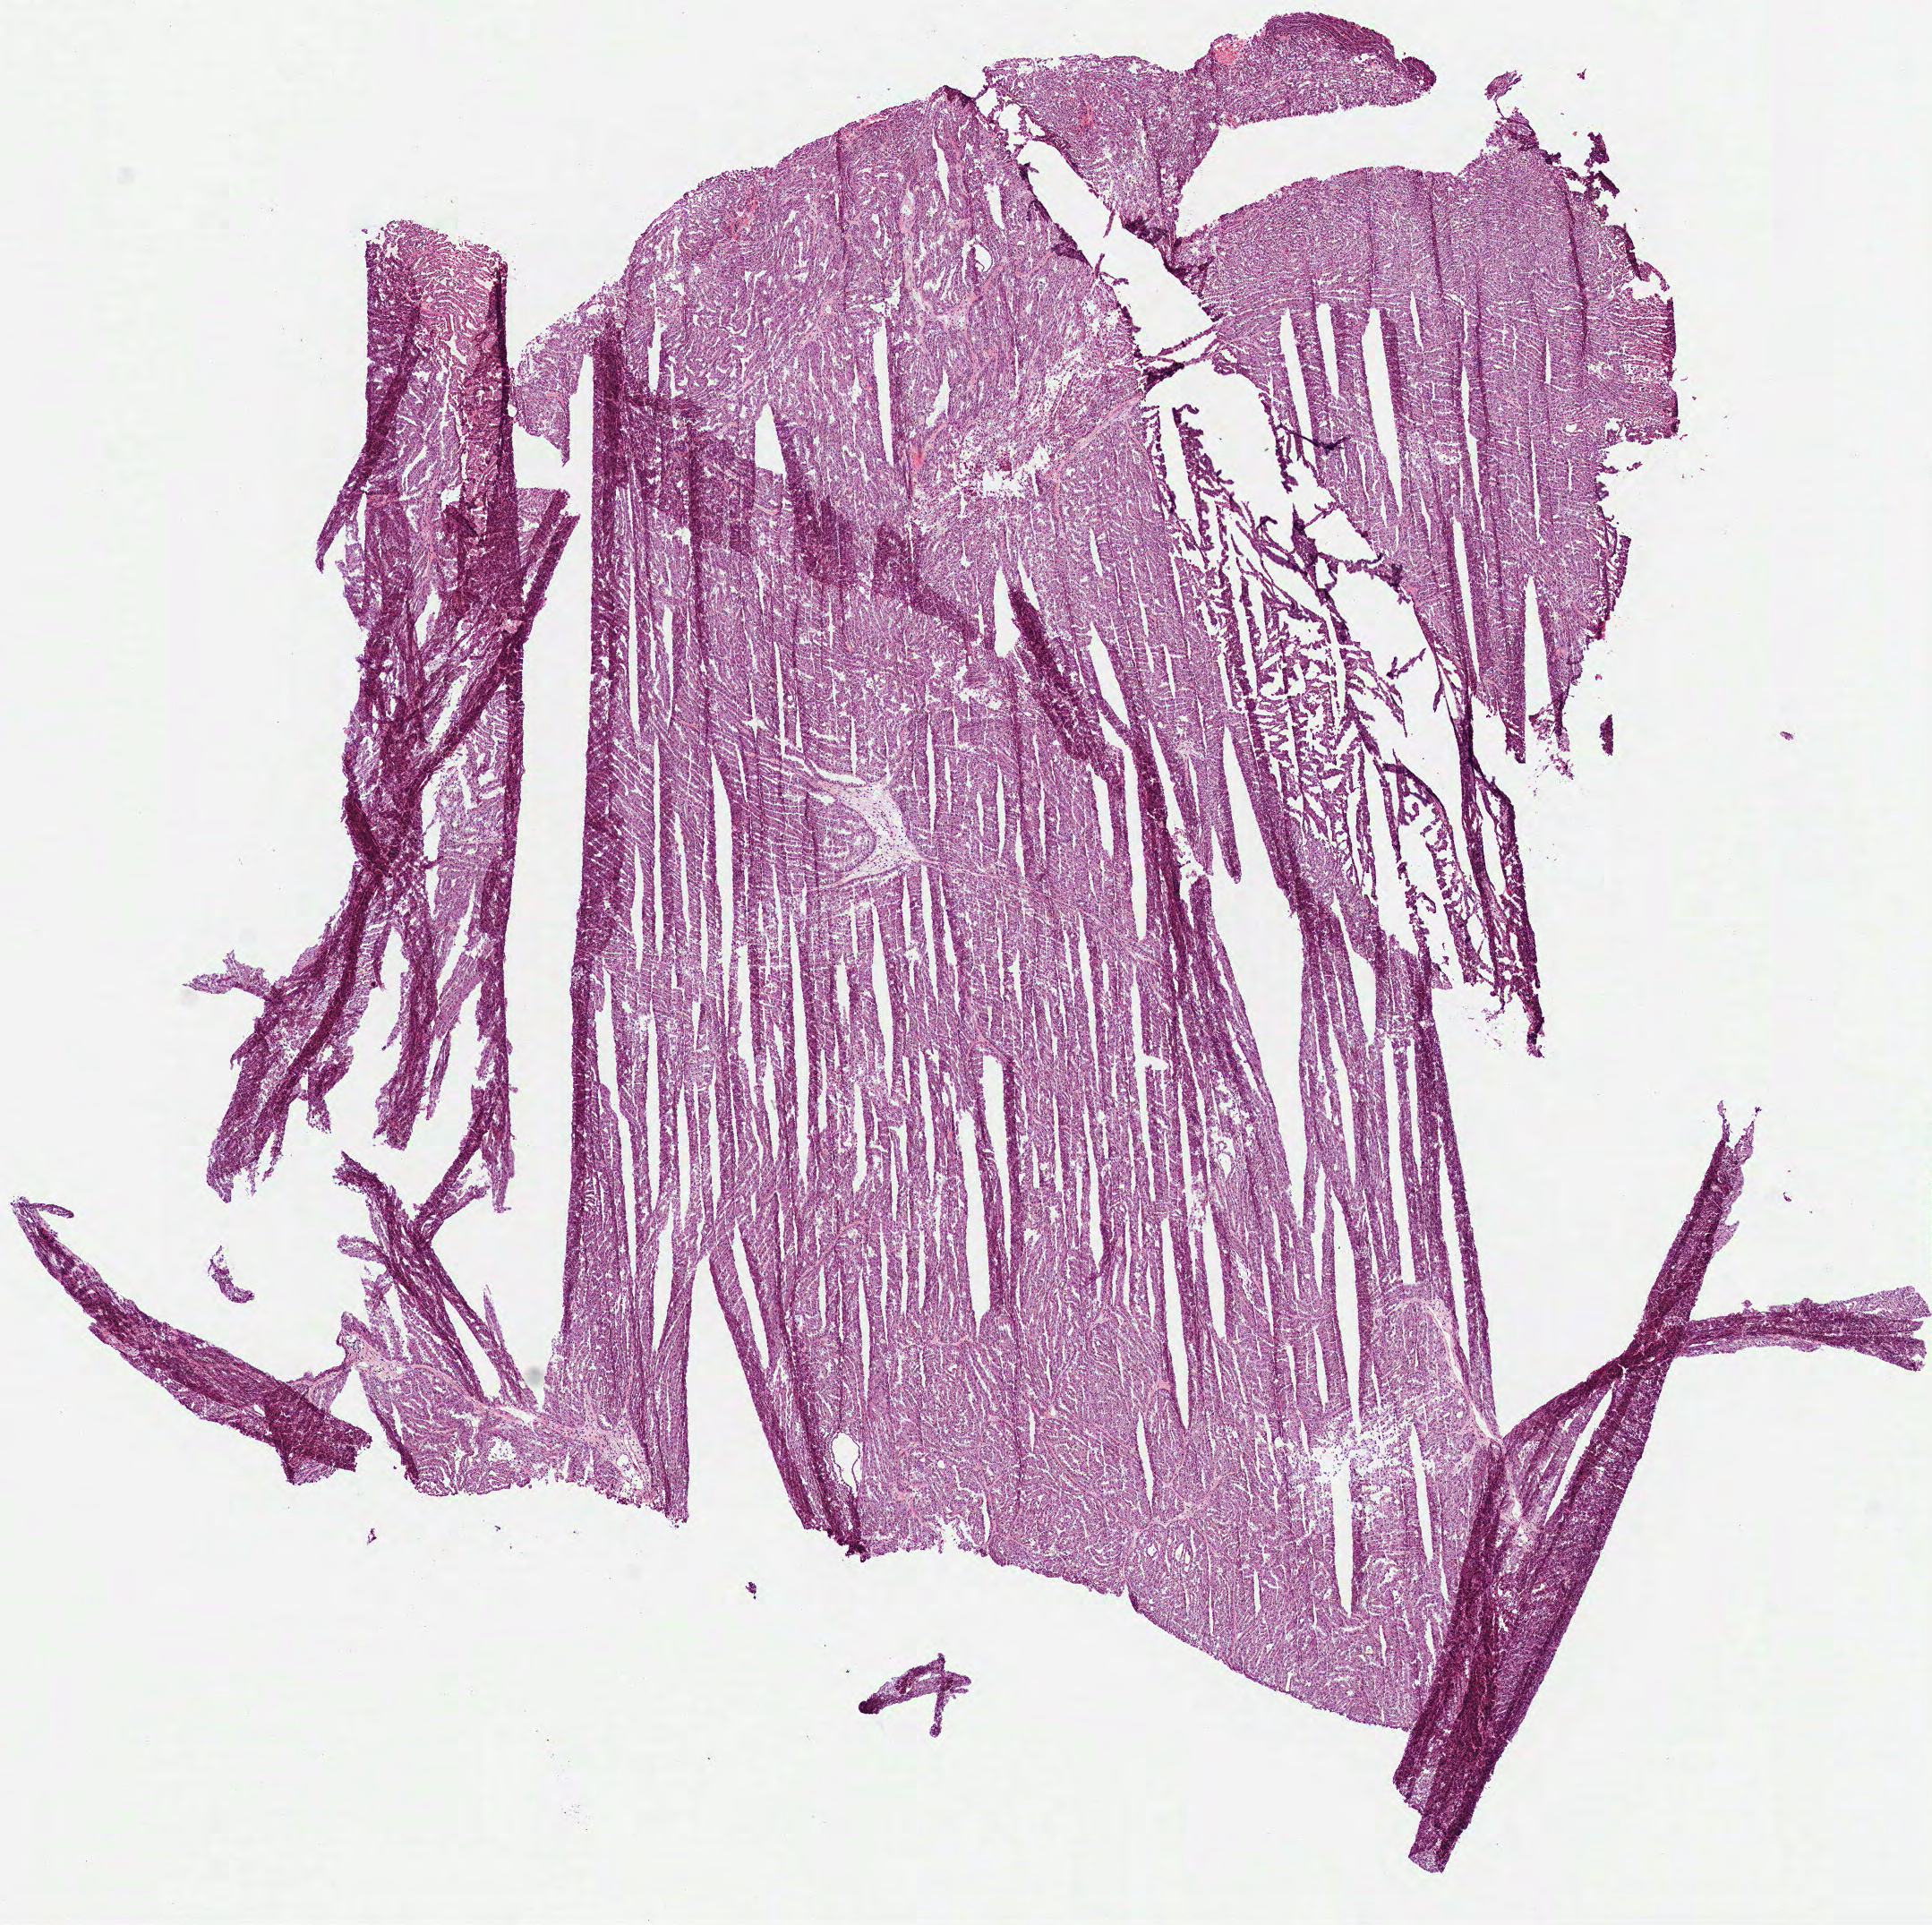
Whole-slide histology image, Hematoxylin and eosin (H&E) stained — low-resolution overview of the scanned area, about 8.7 x 8.7 mm. Frozen section from the top of the tissue portion. Kidney, primary tumour sample. Male, age 63 years at initial diagnosis. Slide review estimates, as recorded: tumour cells 95%, tumour nuclei 95%, normal cells 0%, stromal cells 5%, necrosis 0%.
Diagnosis: Papillary adenocarcinoma, NOS. AJCC pathologic stage: I (7th edition).